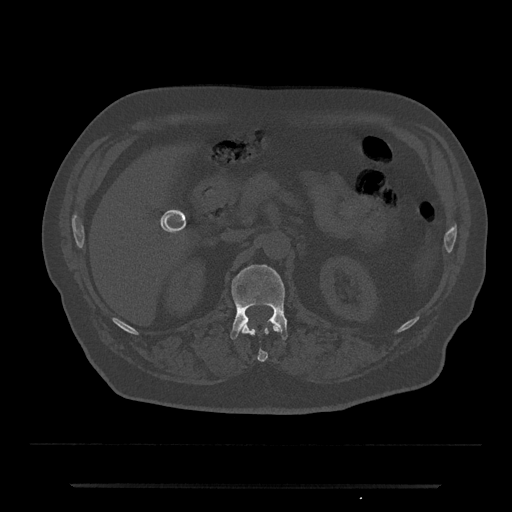
CT including the spine, one axial slice; slice 554 of 797 in the series (ordered by position); reconstruction kernel Br40s/3; 120 kVp; bone window (W 1800 / L 400 HU); 0.5 mm slice thickness; 512 × 512 image matrix, field of view 434 × 434 mm. Male patient, age 80 years. From the clinical record (not read from this slice): primary cancer: prostate; vertebrae with lytic lesions (as recorded): L1, T11.
Outlined on this slice (semi-automatic segmentation, software-assisted and operator-edited):
- L1 vertebra: box from (x=230, y=265) to (x=288, y=340) px
- T12 vertebra: (x=241, y=324)–(x=280, y=362)